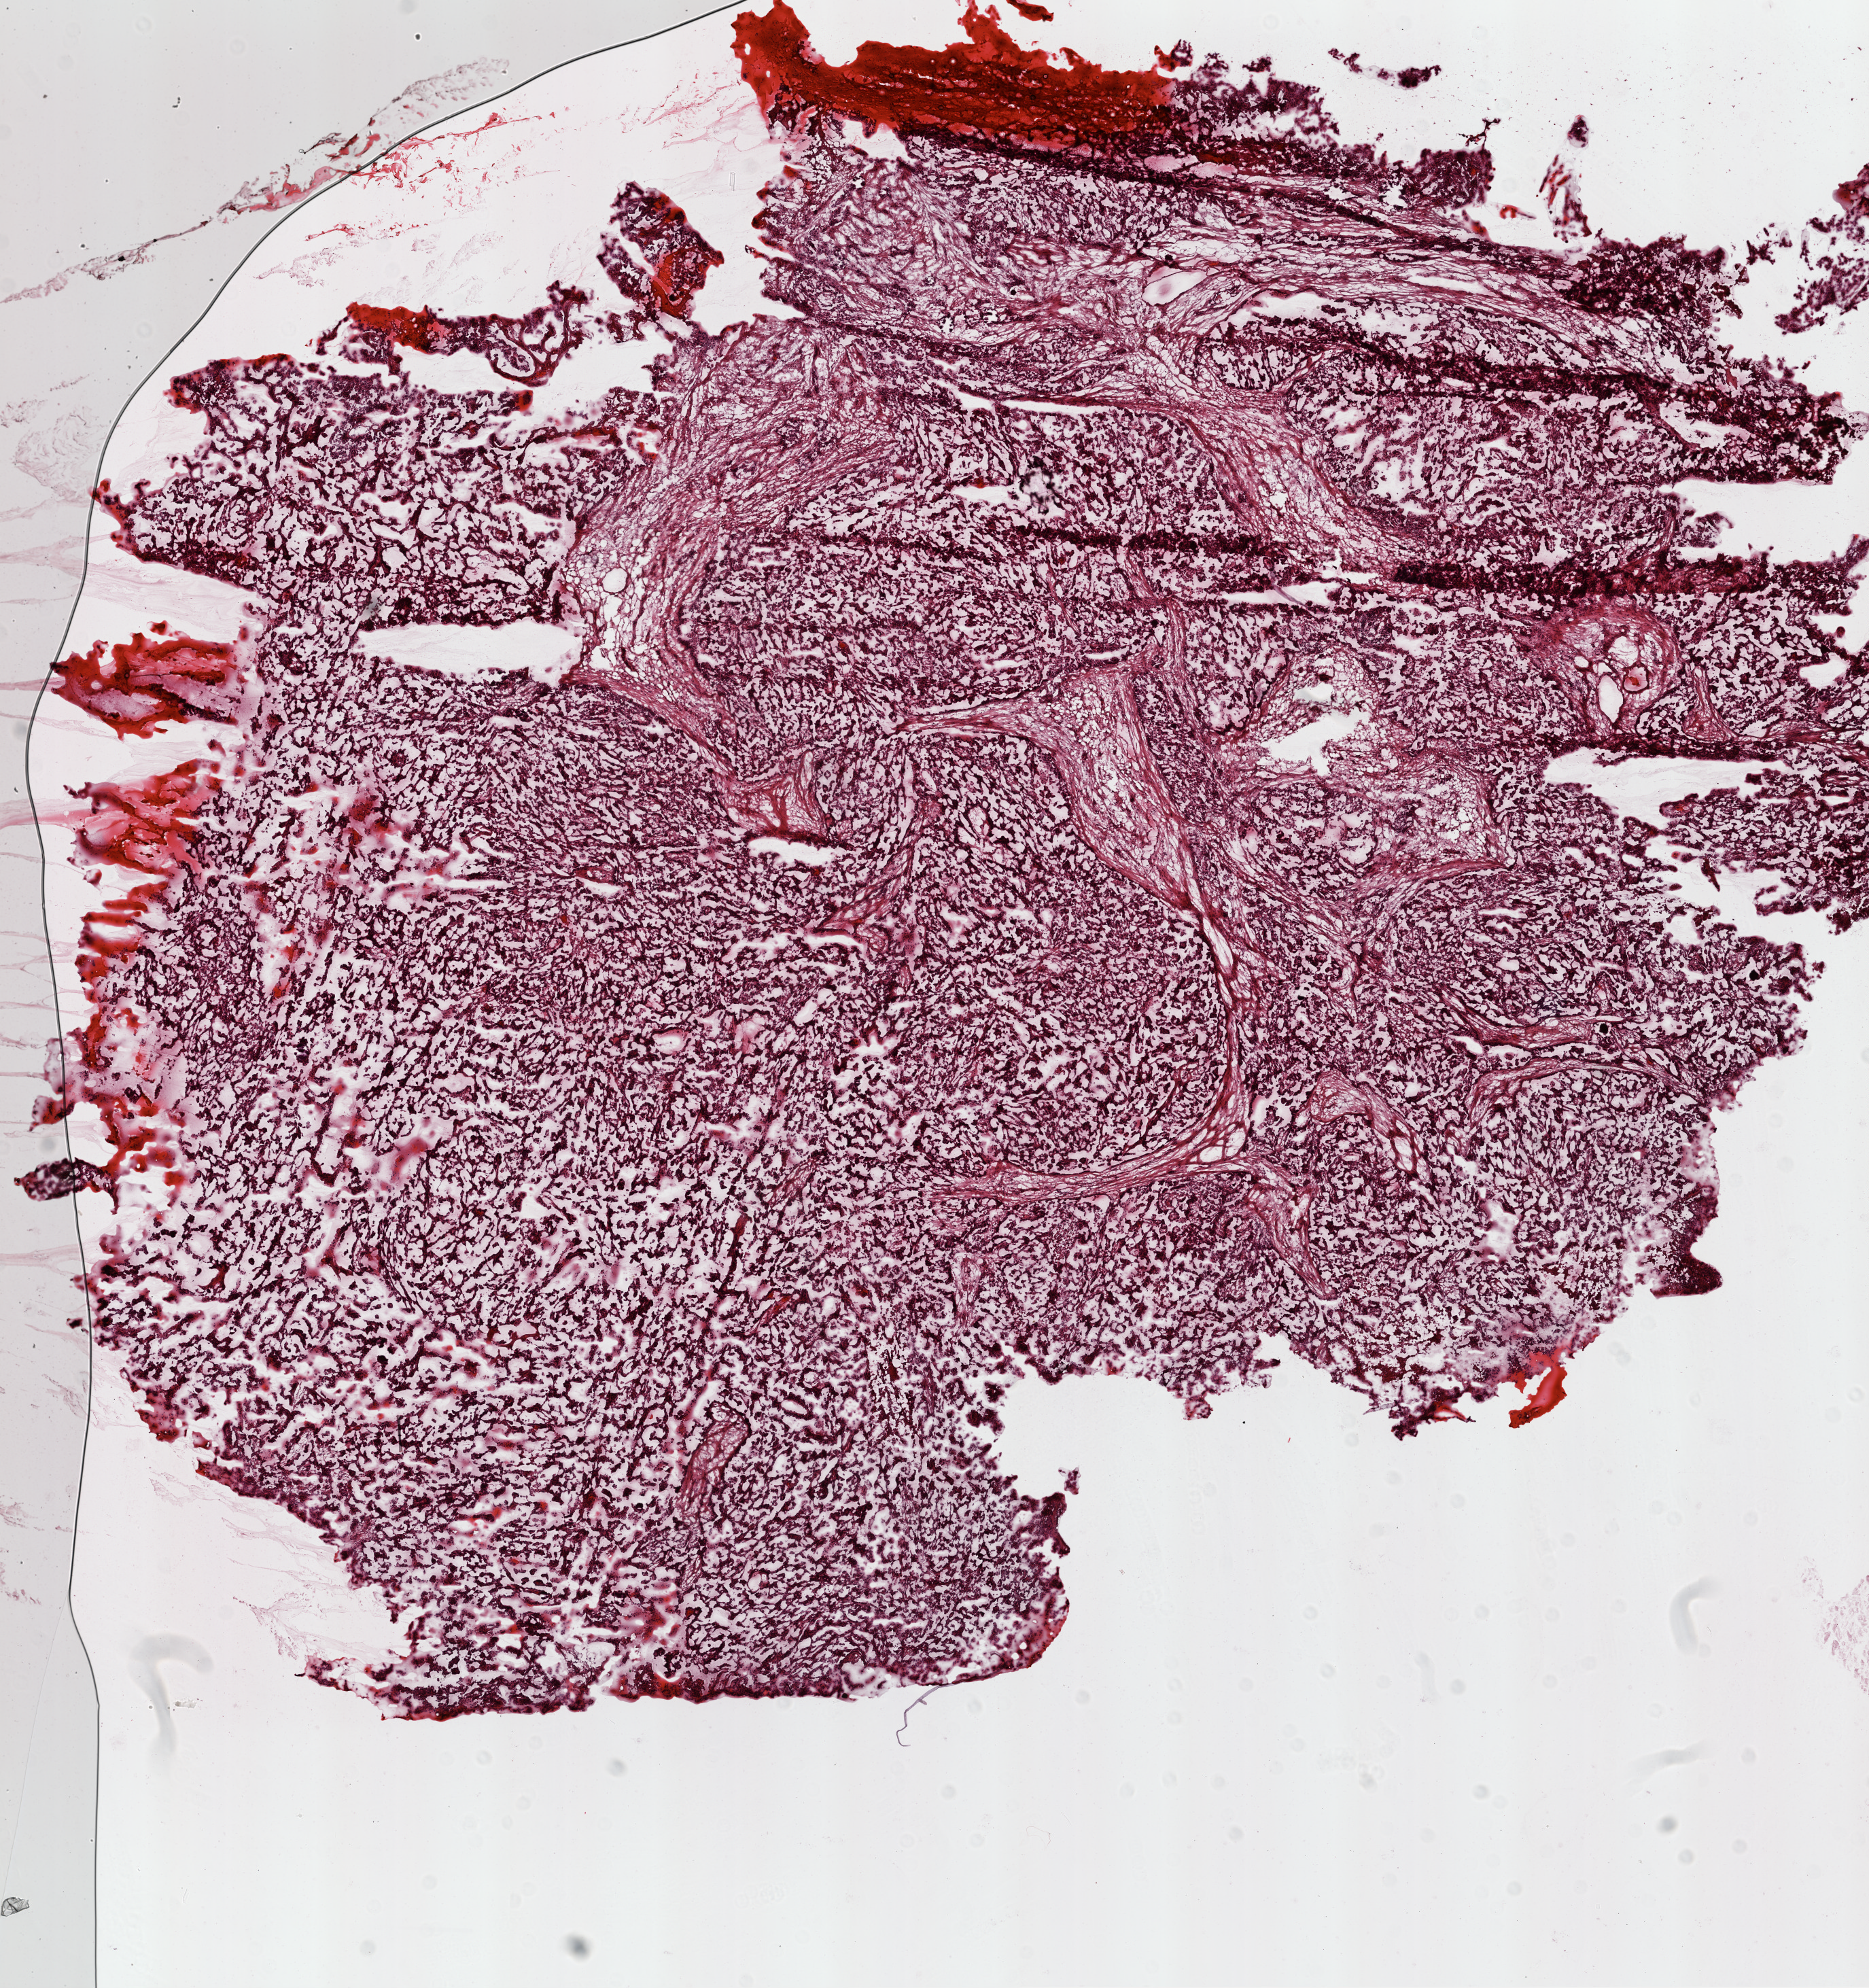
Digitized H&E-stained tissue section (whole slide), a low-resolution overview of the entire scanned area, about 11.0 x 11.7 mm (acquisition: 20x scan), frozen section from the top of the tissue portion, sample: primary tumour, ovary. Female patient; age at initial diagnosis 74 years. Histologic grade: G3 (poorly differentiated). Pathologist review of this section (percent, as recorded): tumour cells 90%, tumour nuclei 90%, normal cells 0%, stromal cells 10%, necrosis 0%. Infiltration values recorded for this section: lymphocyte infiltration 0%, monocyte infiltration 0%, neutrophil infiltration 0%.
Diagnosis: Serous cystadenocarcinoma, NOS. FIGO stage: IIIC.